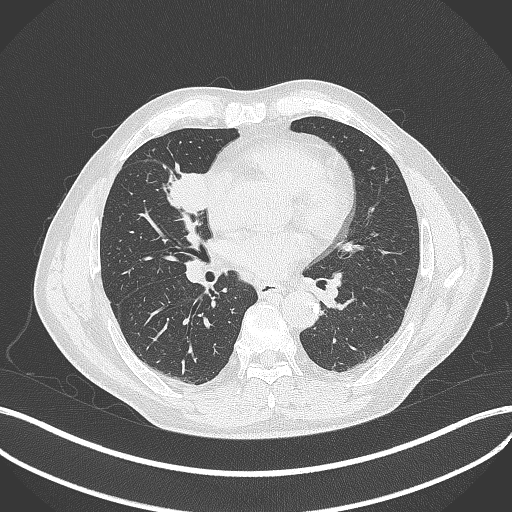
Chest CT, one axial slice; slice 192 of 429 in the series (ordered by position); reconstruction kernel B70f; 120 kVp; lung window (W 1500 / L -600 HU); 1 mm slice thickness; 512 × 512 image matrix, field of view 400 × 400 mm. Patient: male, 61 years. From the clinical record (not read from this slice): clinical TNM (as recorded): T2b N1 M0.
Outlined on this slice (bounding box drawn by a radiologist):
- lung tumour (recorded histology: squamous cell carcinoma): box from (x=164, y=159) to (x=208, y=221) px